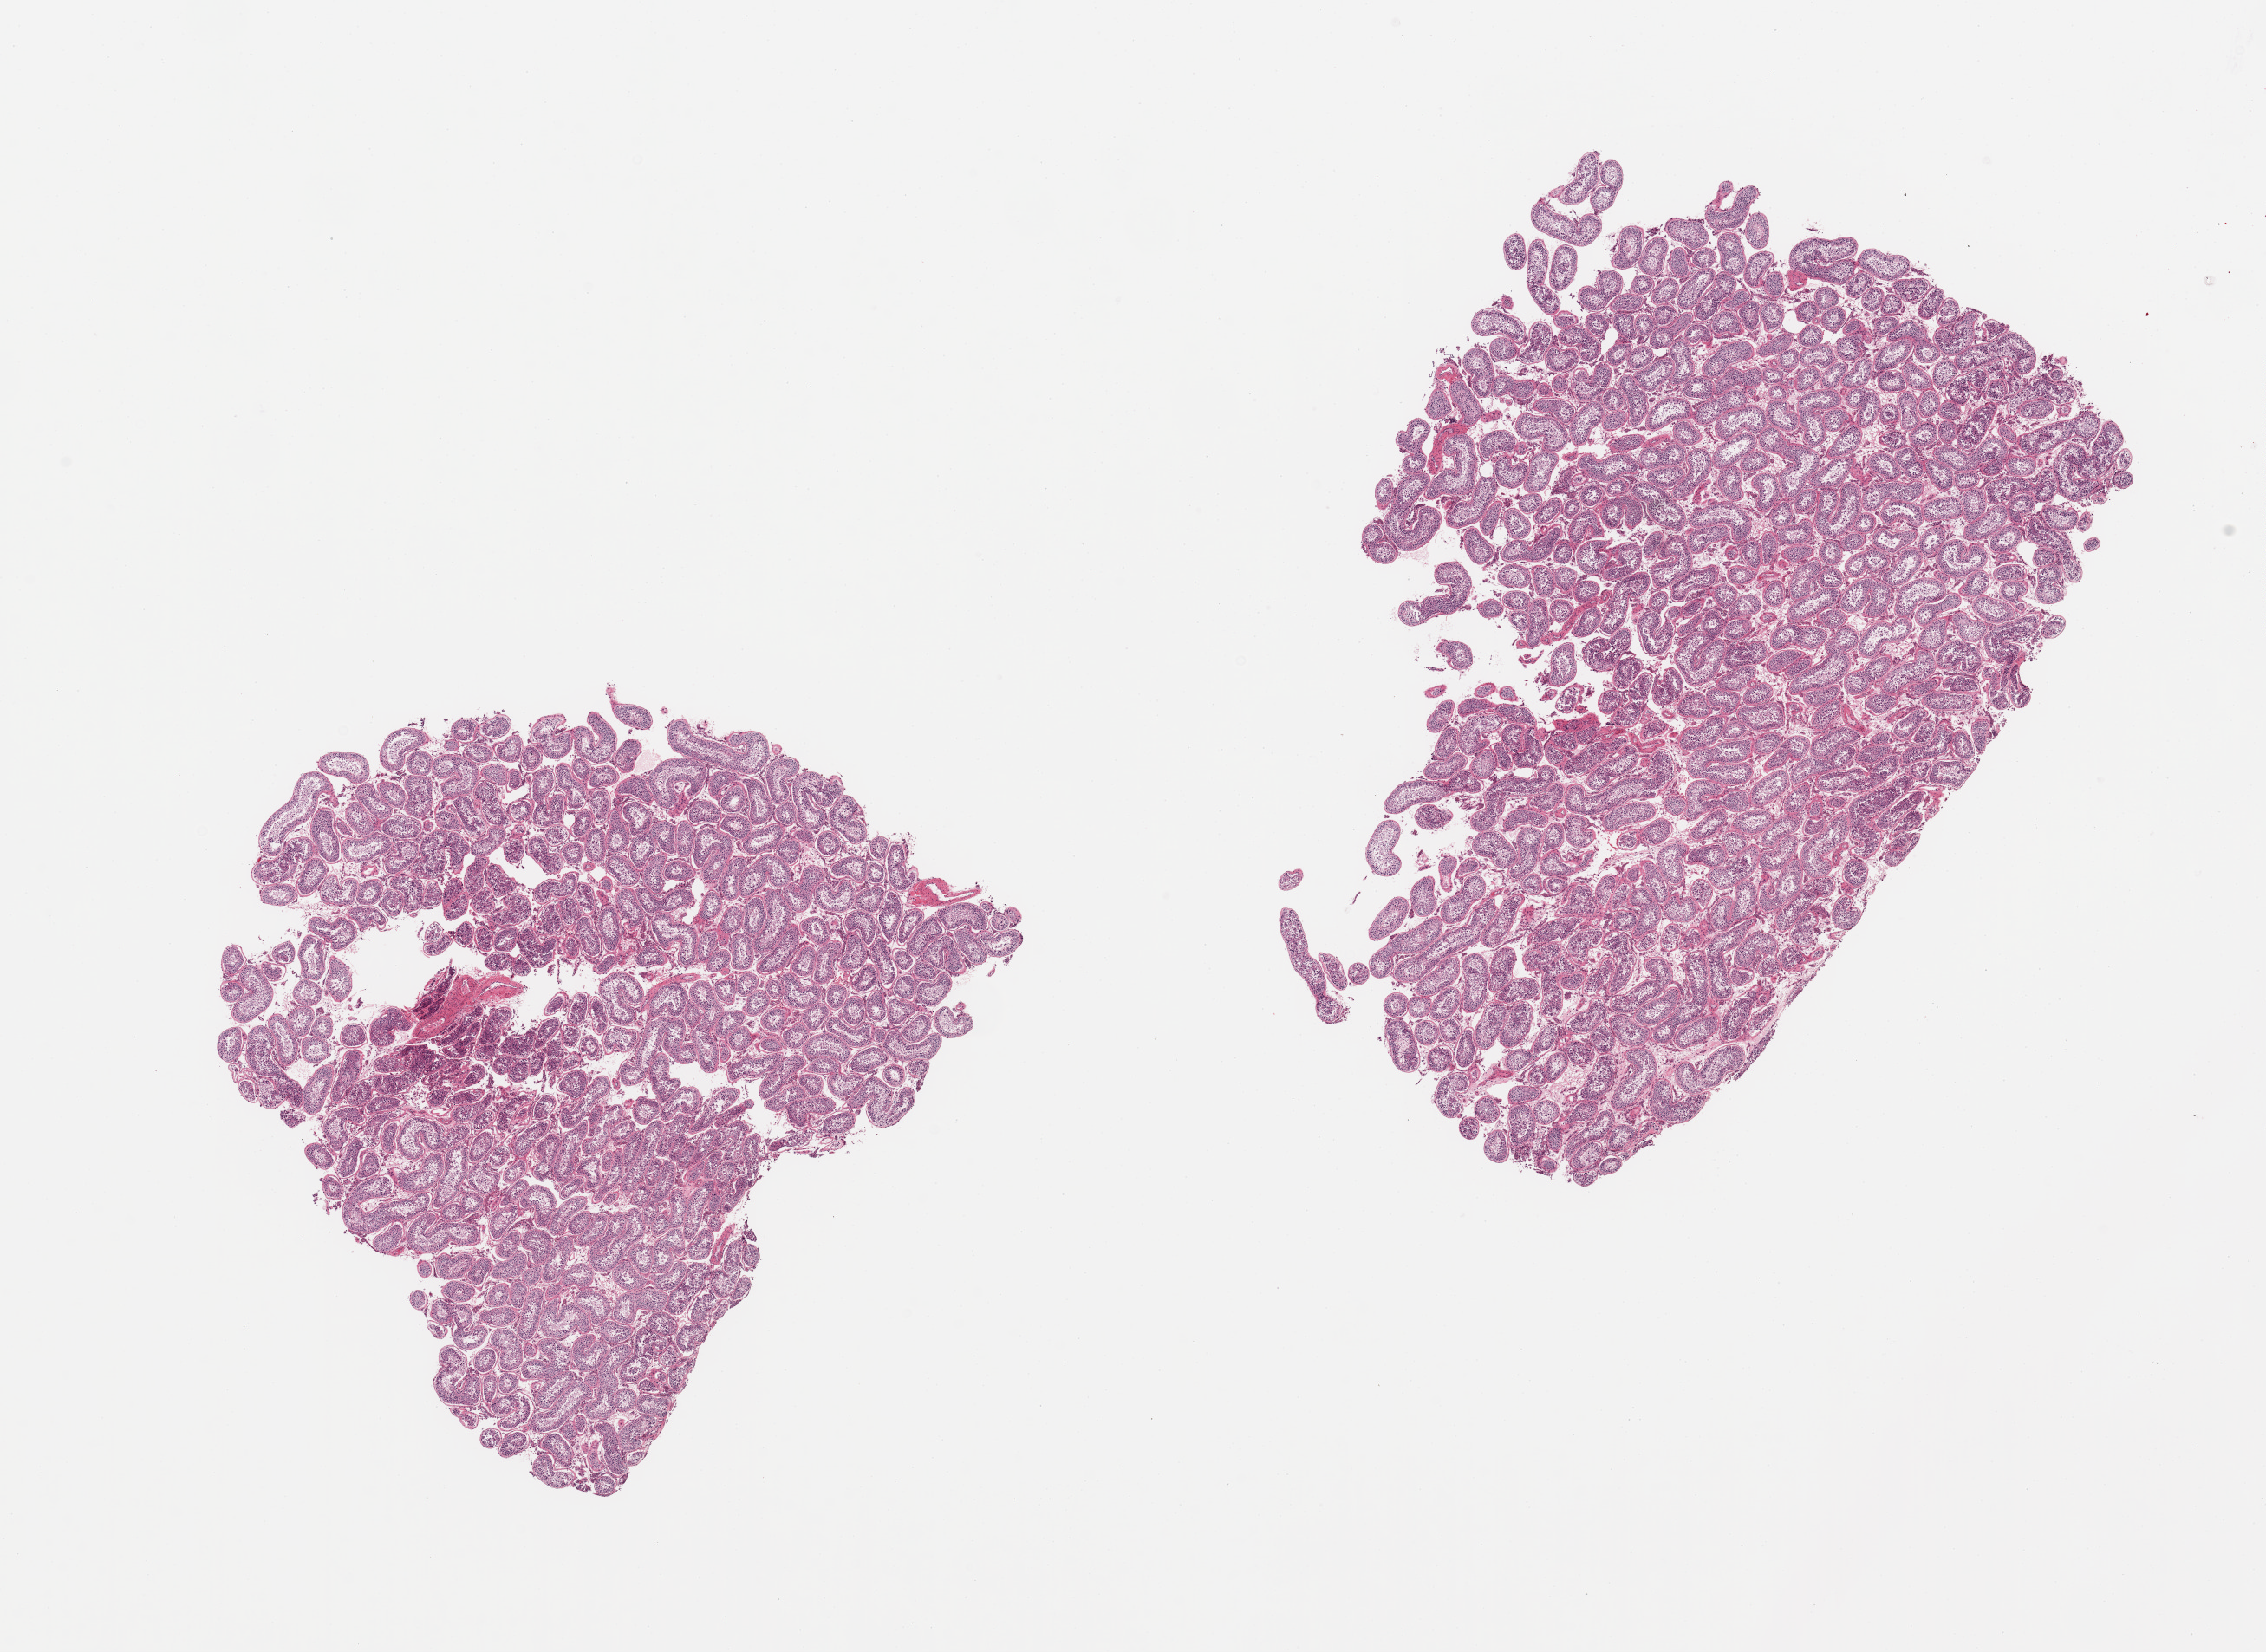
H&E whole-slide image, a low-resolution overview of the entire scanned area, about 20.7 x 15.1 mm (slide scanned at 20x), PAXgene-fixed paraffin-embedded (PFPE) section, section of testis (target tissue), donor tissue sample. Donor sex: male.
* reviewer comment on this tissue sample: 2 pieces, spermatogenesis is present